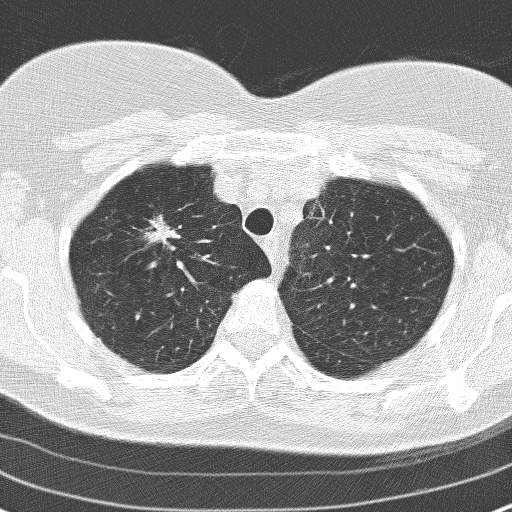
Chest CT (low-dose screening protocol), one axial image; second annual screen; lung window (W 1500 / L -600 HU); lung (sharp) reconstruction kernel (D); slice 34 of 160 in the series. Female participant, aged 60 years at enrolment.
• Expert reader's lesion annotation, bounding box (x1, y1, x2, y2) in pixels: (125, 208, 179, 257).
• The exam's reader record, not a measurement of the box and not confirmed to be the same lesion: non-calcified nodule or mass ≥4 mm, right upper lobe, 17 × 15 mm, spiculated (stellate) margins, soft tissue attenuation, pre-existing on the prior screen: yes; interval growth: yes.
• Participant outcome: lung cancer diagnosed 78 days after this screen — adenocarcinoma, NOS, right upper lobe, moderately differentiated (G2), stage IA (AJCC 6th edition), 23 mm at pathology.